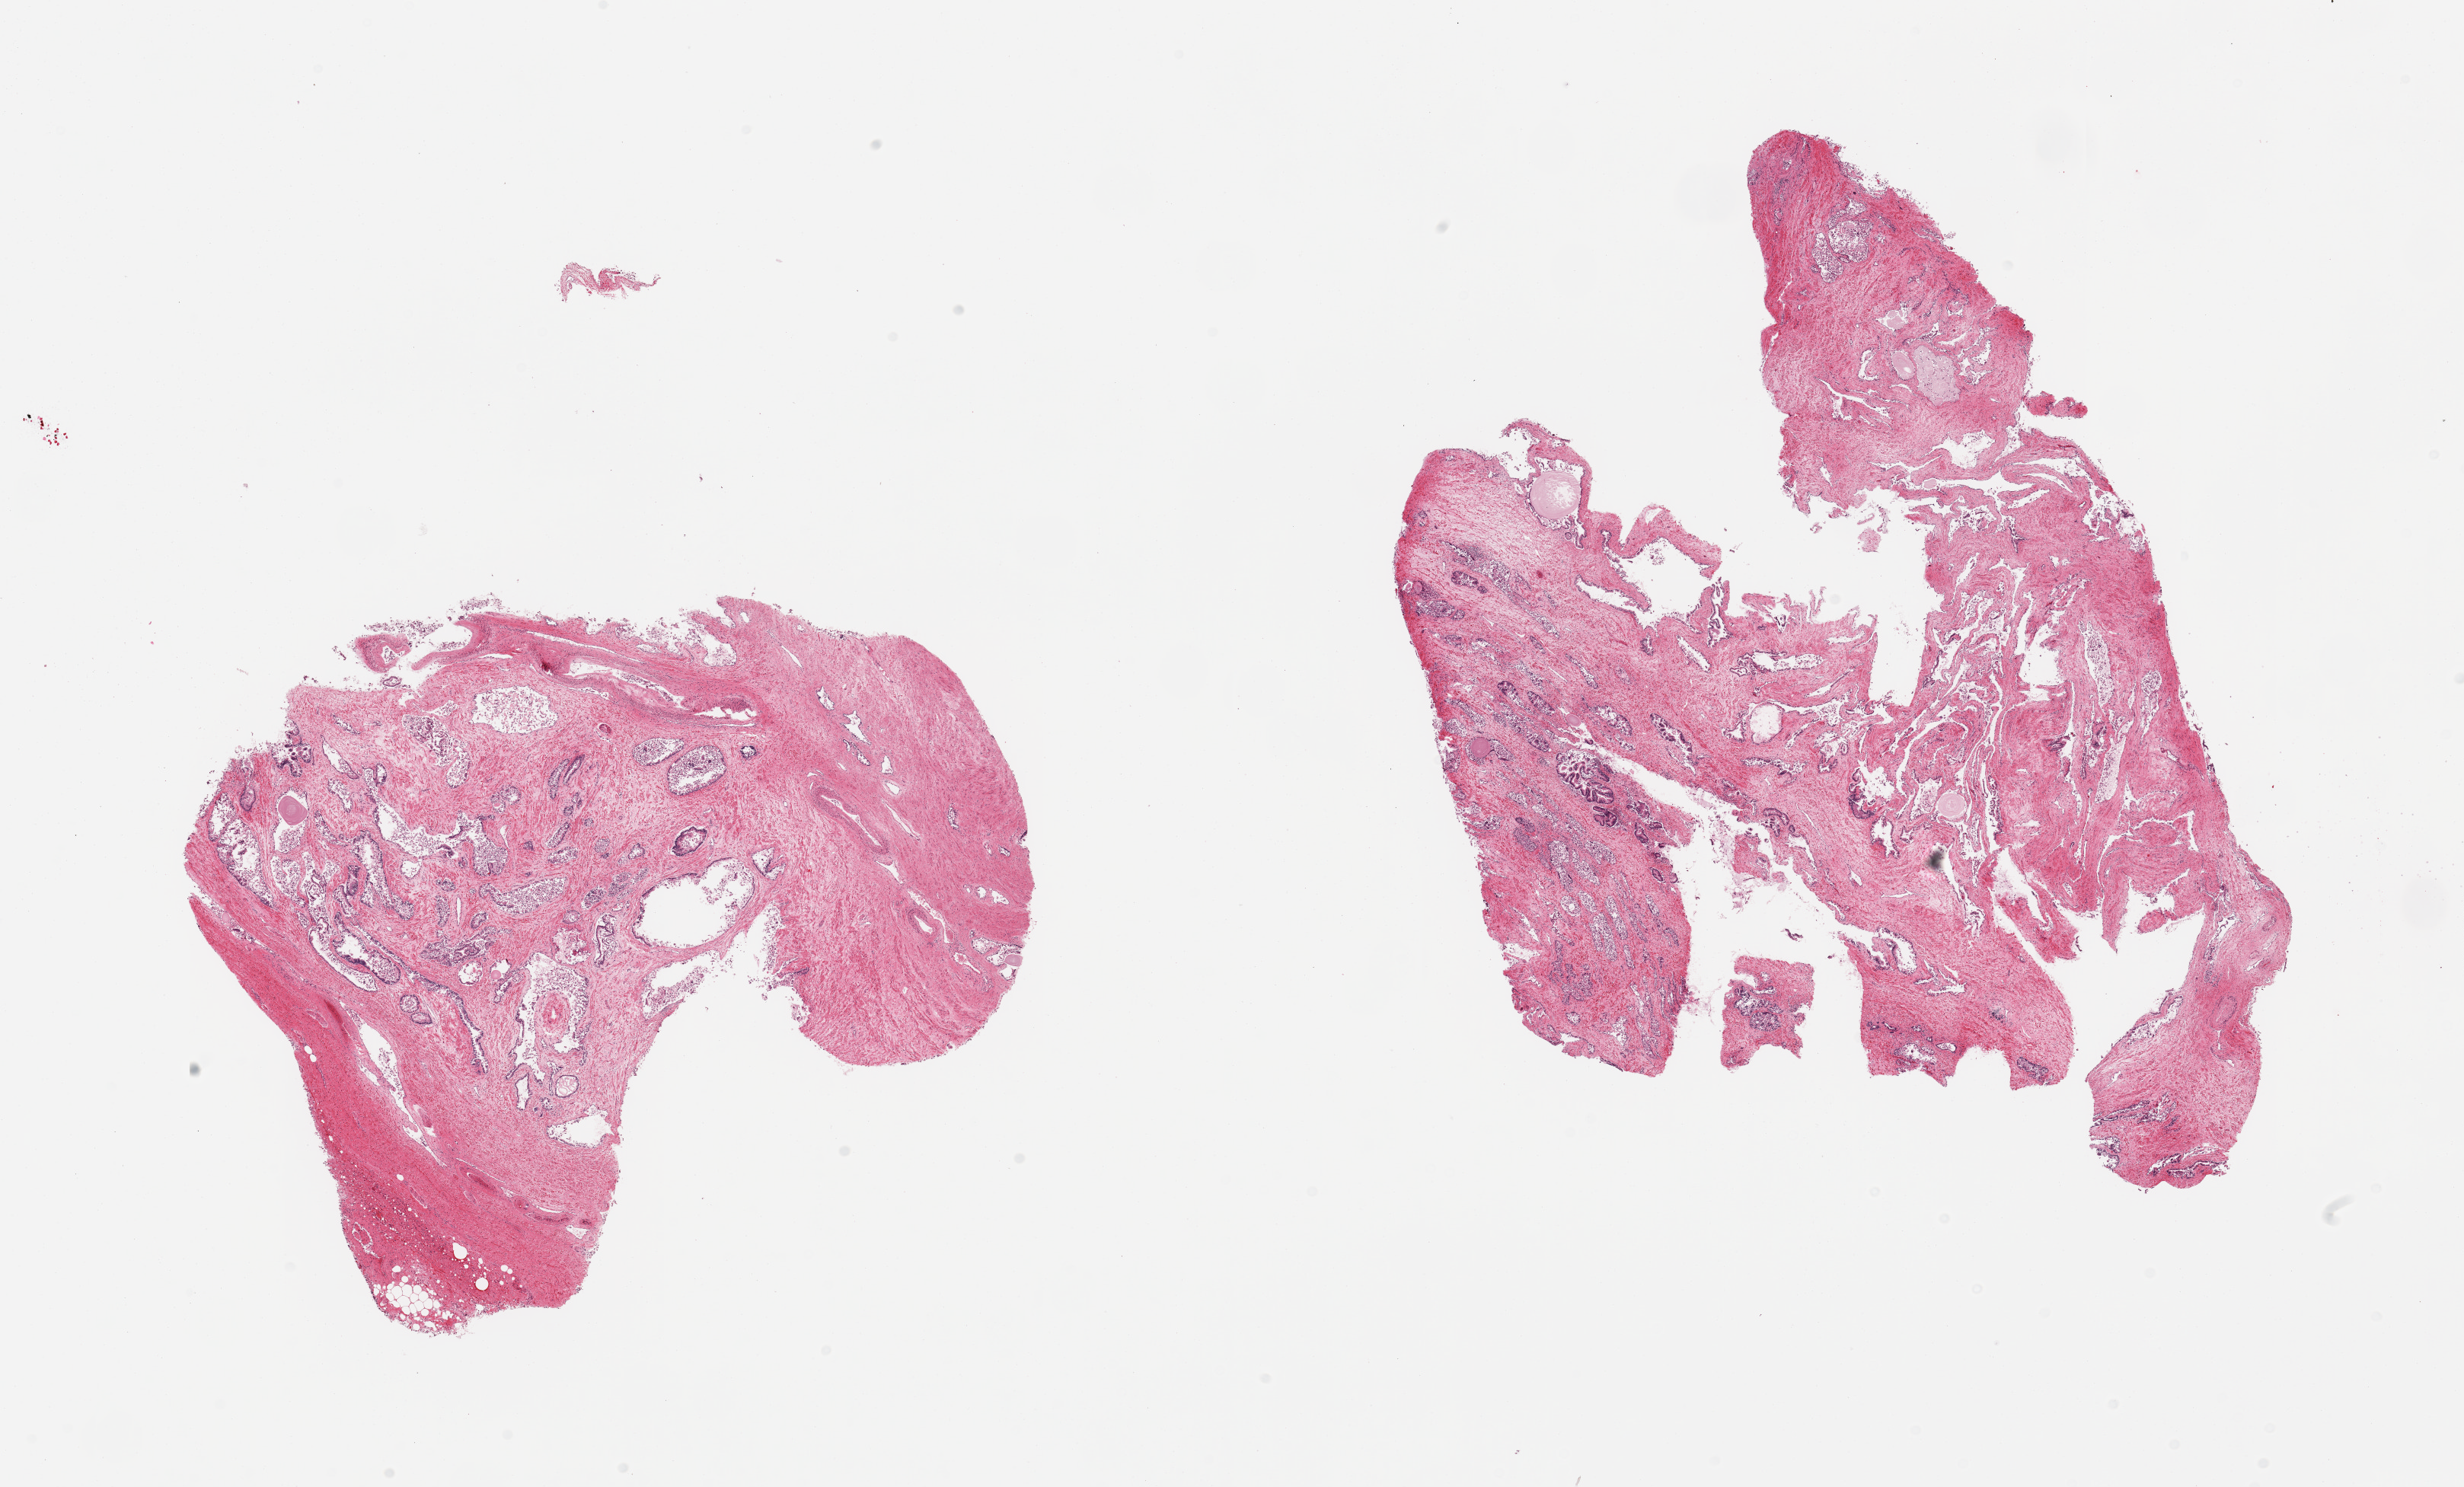
Digitized H&E-stained section, brightfield, whole scanned area (about 25.6 x 15.4 mm) shown as a low-resolution overview. PAXgene-fixed paraffin-embedded (PFPE) section. Target tissue: prostate. Tissue donor sample. Donor sex: male.
Reviewer comment on this tissue sample: 2 pieces; glands sloughed.